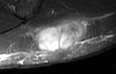
MRI of an extremity soft-tissue mass, one axial slice. Position 15 of 36 along the scan axis. STIR. MR volume resampled by the dataset authors to the PET/CT grid (not the native acquisition matrix). 3.27 mm slice thickness. 116 × 74 image matrix. Male patient. Case-level facts recorded for this patient, not image findings: histological type: pleiomorphic leiomyosarcoma; grade: high; site of the primary tumour: left buttock.
Outlined on this slice (expert contour drawn on MRI and transferred to this co-registered scan by the dataset authors):
- gross tumour volume including surrounding oedema: bounding box [x1, y1, x2, y2] px = [28, 17, 85, 54]
- gross tumour volume (mass): [32, 19, 83, 54]